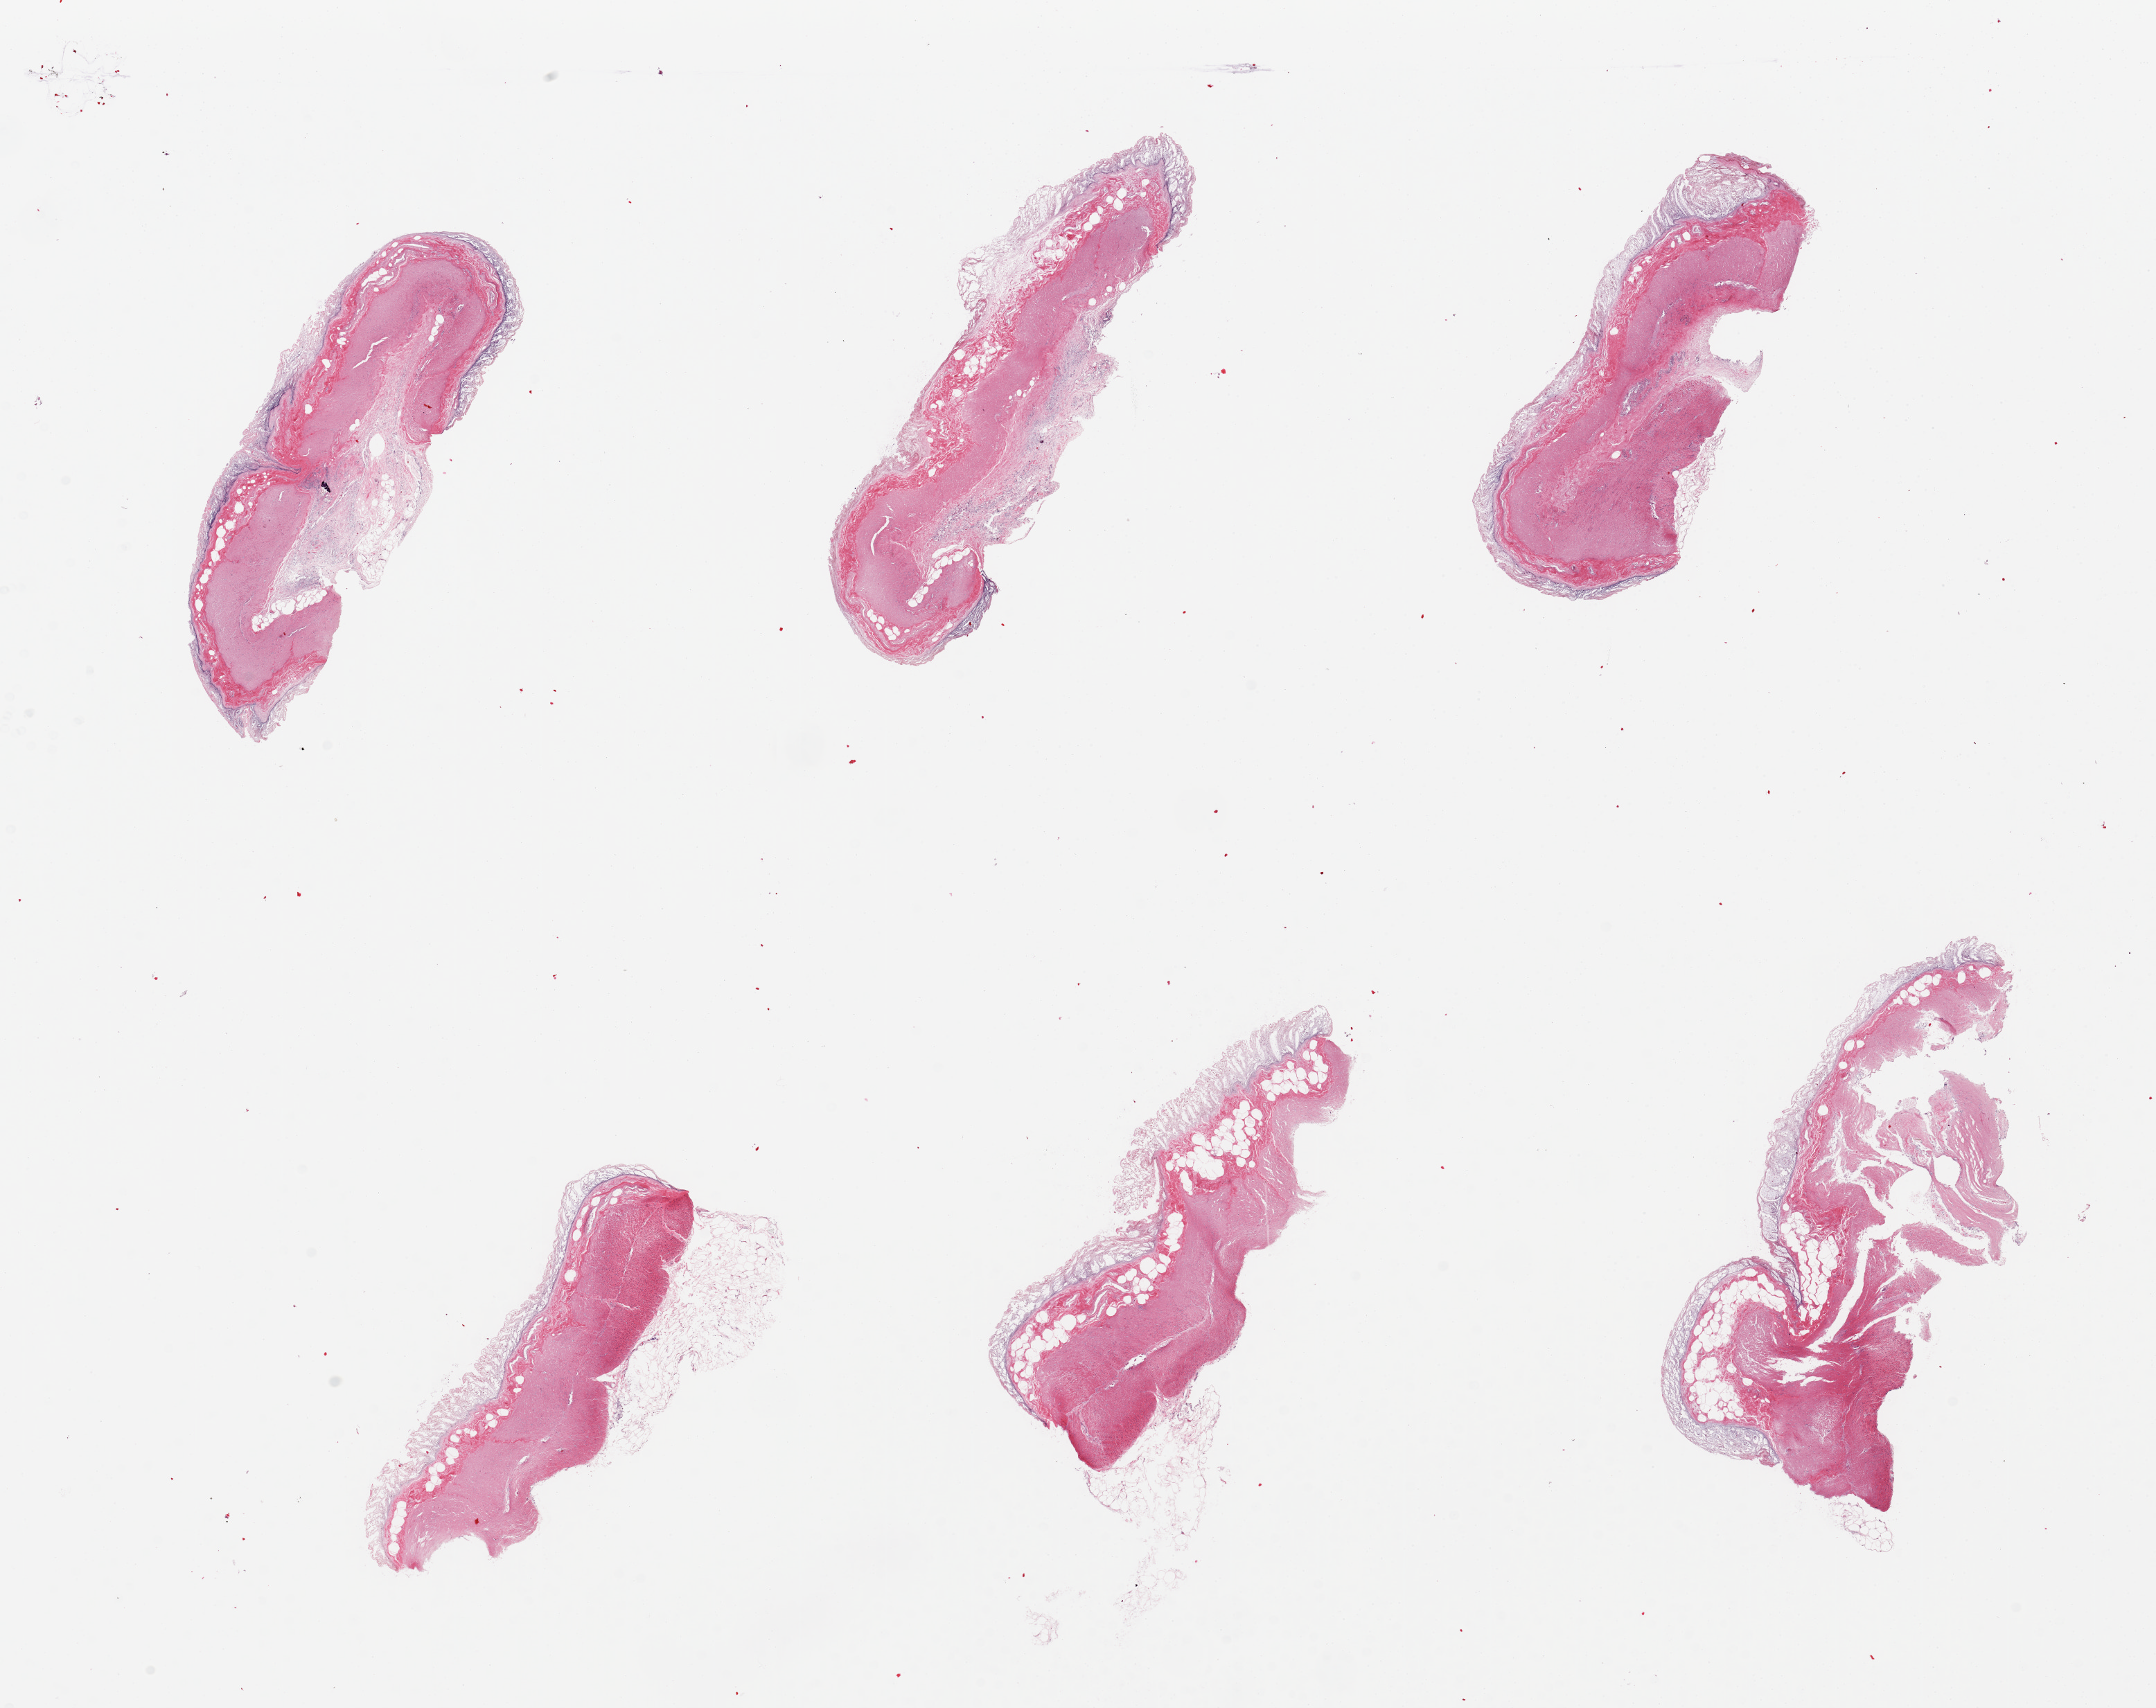
Whole-slide image, haematoxylin and eosin stain, whole scanned area (about 24.6 x 19.5 mm, from a 20x scan) shown as a low-resolution overview; PAXgene-fixed paraffin-embedded (PFPE) section; target tissue: transverse colon; tissue donor sample. Female donor.
Pathologist's review note for this sample: 6 pieces, mucosa totally autolyzed.